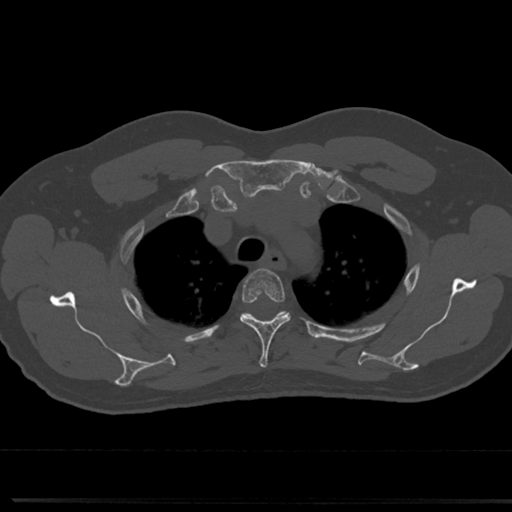
CT including the spine, one axial slice. Position 583 of 817 along the scan axis. Reconstruction kernel Br40s/3. 120 kVp. Bone window (W 1800 / L 400 HU). 0.5 mm slice thickness. 512 × 512 image matrix, field of view 355 × 355 mm. Patient: male, 61 years. Case-level facts recorded for this patient, not image findings: primary cancer: prostate.
Outlined on this slice (semi-automatically segmented with operator editing):
- T3 vertebra: box from (x=239, y=270) to (x=290, y=369) px
- T4 vertebra: (x=222, y=310)–(x=308, y=342)